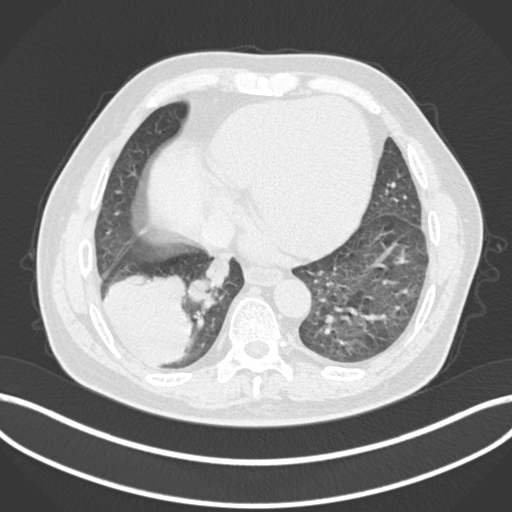
Chest CT, one axial slice; position 44 of 200 along the scan axis; reconstruction kernel B30f; 120 kVp; lung window (W 1500 / L -600 HU); 512 × 512 image matrix, field of view 400 × 400 mm. Male patient, age 59 years.
Annotated regions visible in this slice (rectangle marked by the reading radiologist):
- lung tumour (recorded histology: adenocarcinoma): bounding box [x1, y1, x2, y2] px = [101, 267, 193, 371]